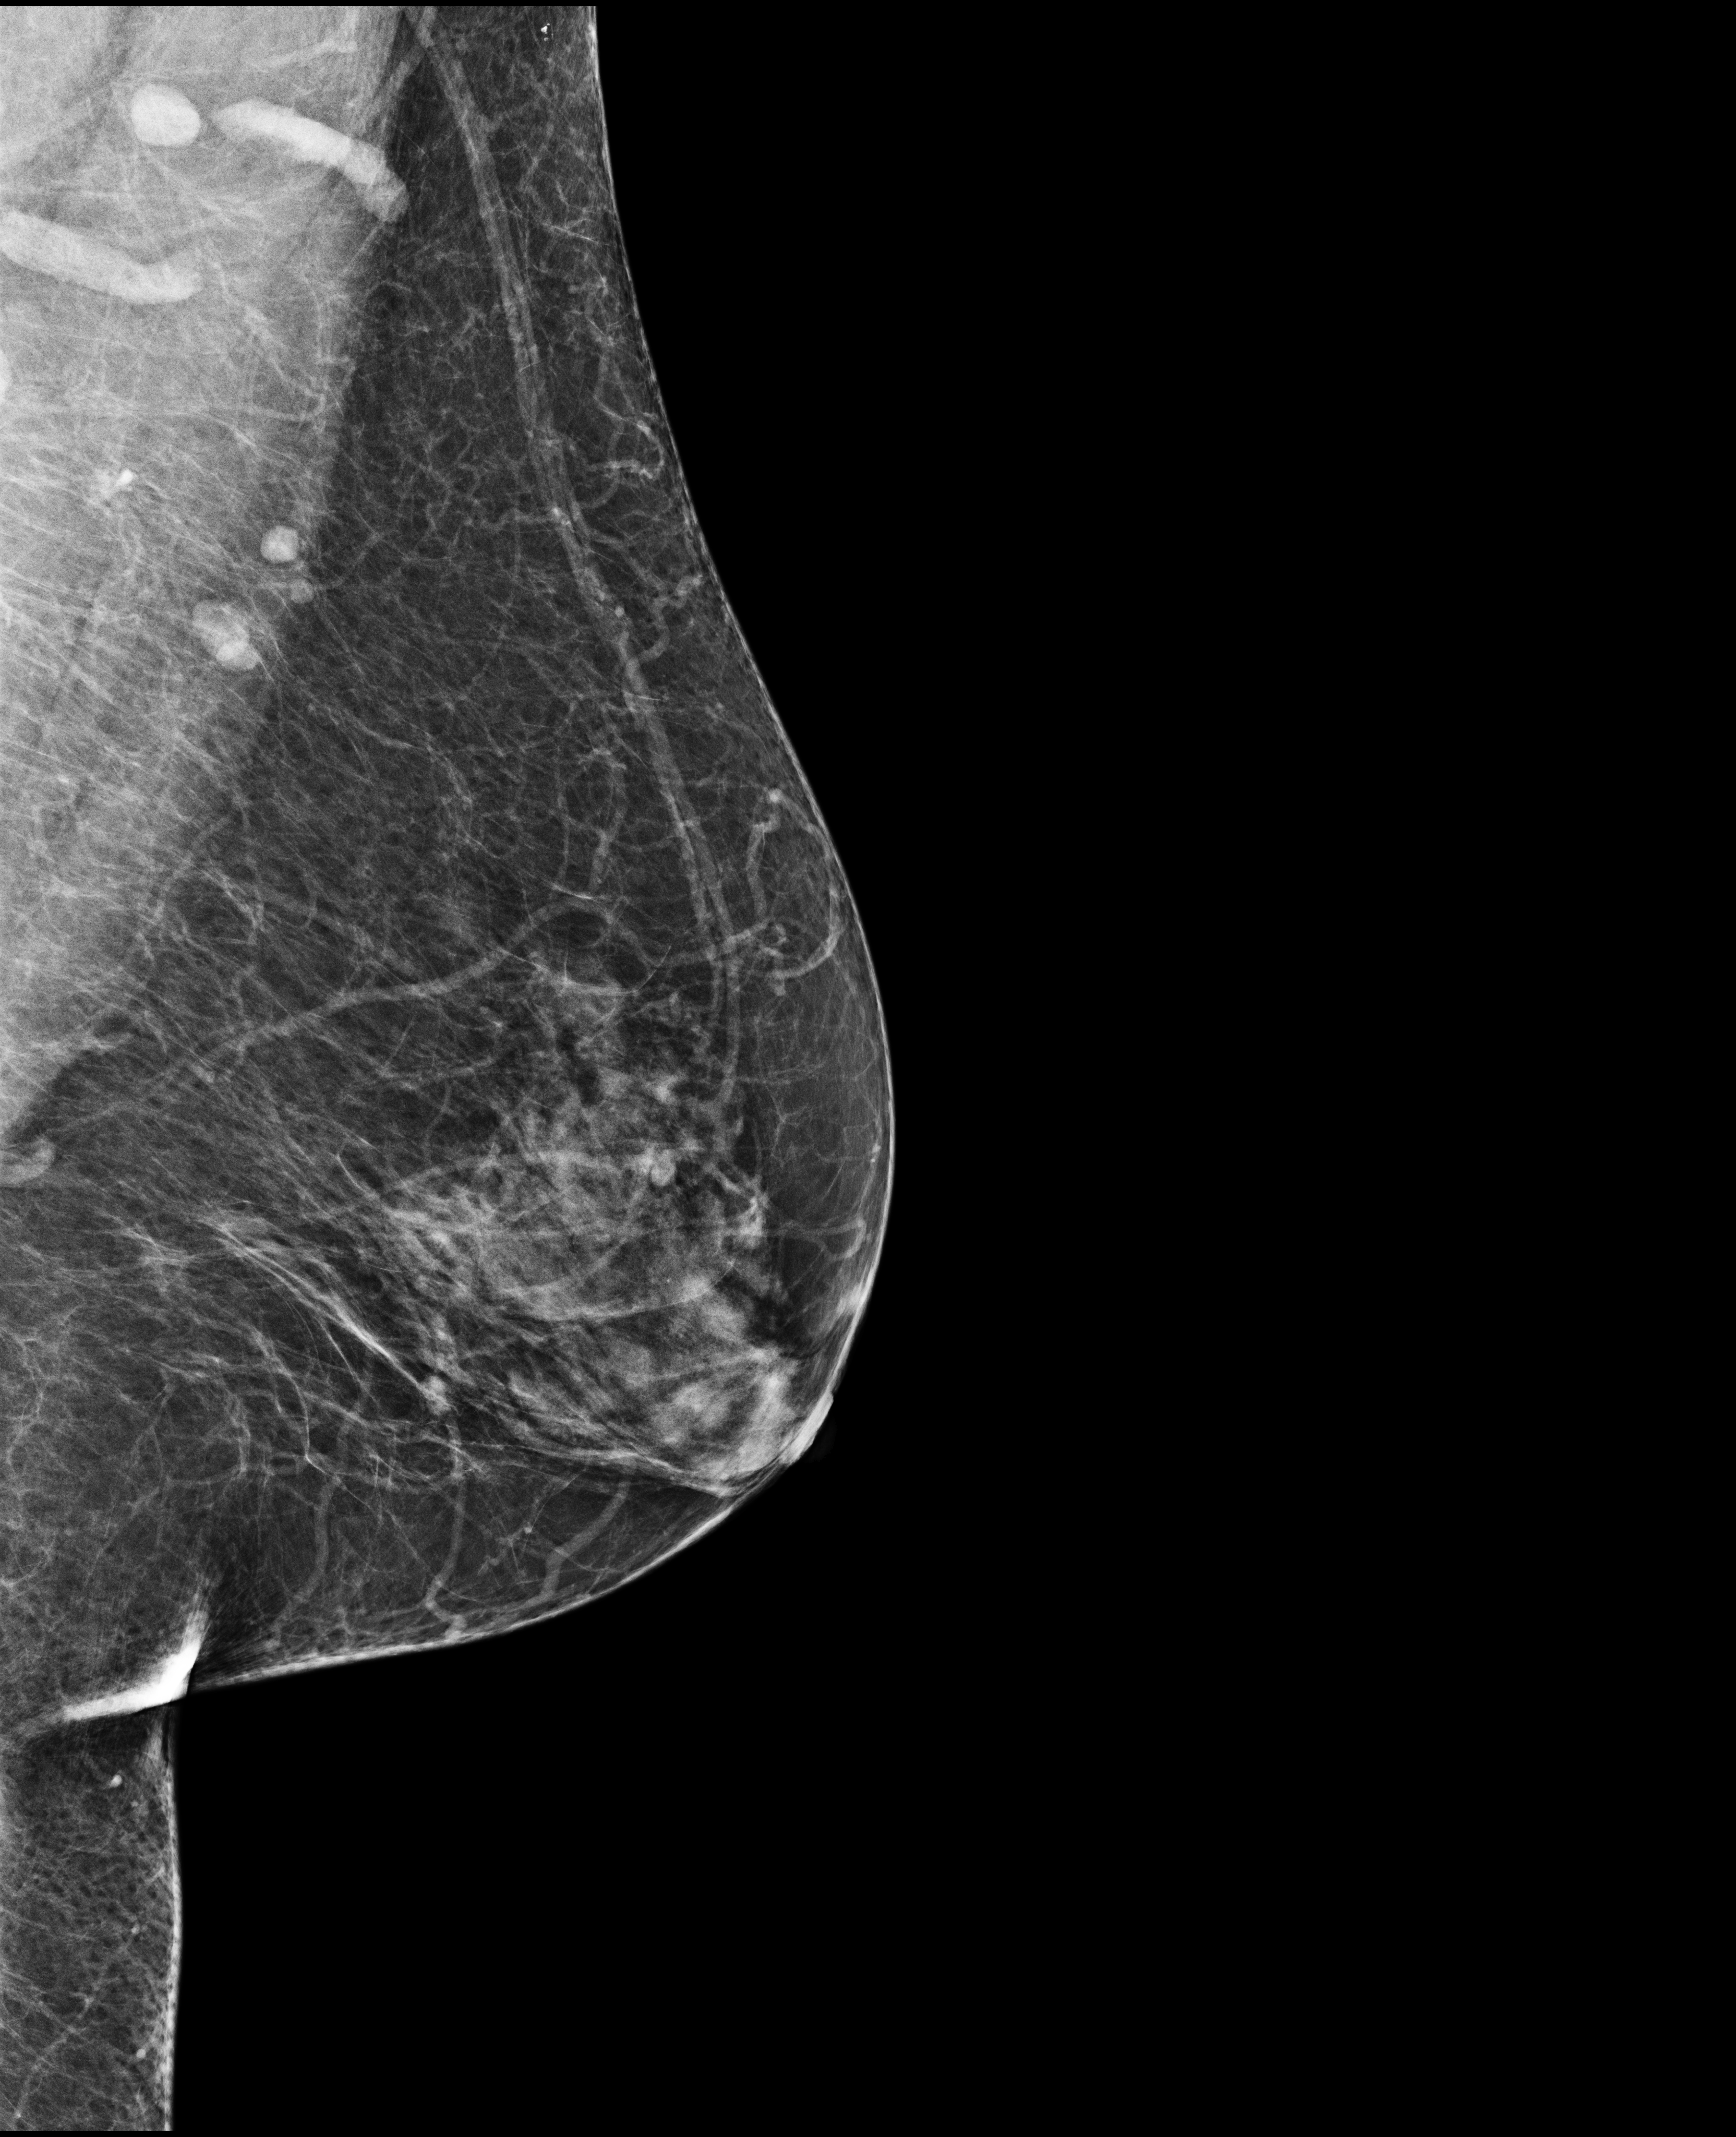
Screening examination; compressed breast thickness 53 mm.
Image type: full-field digital mammogram. Breast: left. Projection: medio-lateral oblique projection.